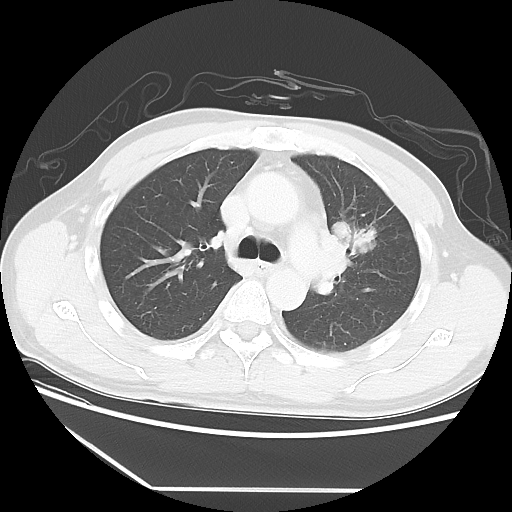
Chest CT, one axial slice. Slice 37 of 56 in the series (ordered by position). Lung window (W 1500 / L -600 HU). 512 × 512 image matrix, field of view 373 × 373 mm. Patient: male, 53 years. Case-level facts recorded for this patient, not image findings: clinical TNM (as recorded): T2a N1 M1b.
Outlined on this slice (rectangle marked by the reading radiologist):
- lung tumour (recorded histology: adenocarcinoma): bounding box [x1, y1, x2, y2] px = [332, 215, 380, 264]